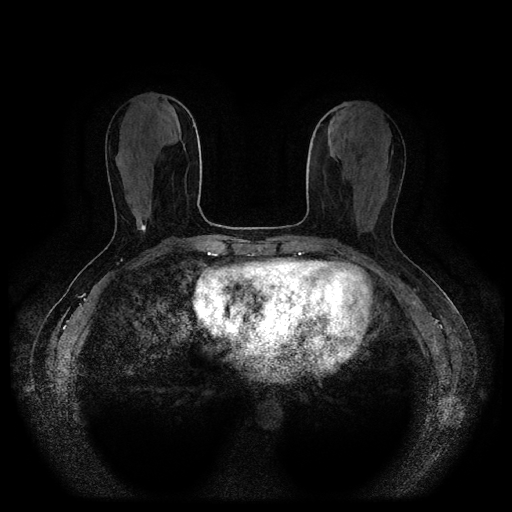
Breast MRI (dynamic contrast-enhanced, multi-phase), one axial slice. Slice 36 of 116 in the series (ordered by position). Dynamic contrast-enhanced series, time point 2 of 5 at this slice position (early post-contrast). 1.5 T. TE 2.6 ms, TR 5.3 ms. 2 mm slice thickness. 512 × 512 image matrix, field of view 360 × 360 mm. Patient: female, 53 years.
Outlined on this slice (semi-automatically segmented with operator editing):
- breast lesion (labelled 'tumour' in the annotation; benign lesions carry a separate 'benign' label): box from (x=135, y=211) to (x=146, y=233) px